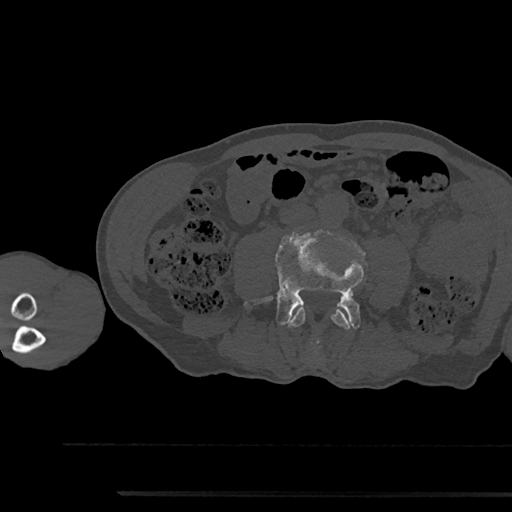
CT including the spine, one axial slice. Slice 438 of 797 in the series (ordered by position). Reconstruction kernel Br40s/3. Bone window (W 1800 / L 400 HU). 0.5 mm slice thickness. 512 × 512 image matrix, field of view 367 × 367 mm. Patient: male, 79 years. From the clinical record (not read from this slice): primary cancer: prostate.
Structures marked on this image (semi-automatically segmented with operator editing):
- L3 vertebra: box from (x=288, y=305) to (x=351, y=330) px
- L4 vertebra: (x=244, y=229)–(x=364, y=348)